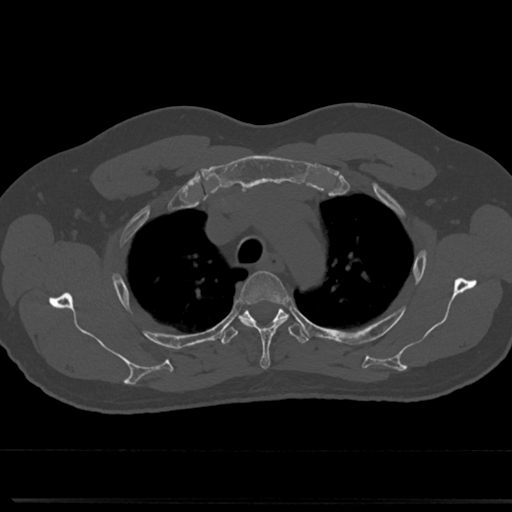
CT including the spine, one axial slice; slice 571 of 817 in the series (ordered by position); 120 kVp; bone window (W 1800 / L 400 HU); 0.5 mm slice thickness; 512 × 512 image matrix, field of view 355 × 355 mm. Patient: male, 61 years. From the clinical record (not read from this slice): primary cancer: prostate.
Structures marked on this image (semi-automatically segmented with operator editing):
- T3 vertebra: bounding box [x1, y1, x2, y2] px = [241, 270, 285, 369]
- T4 vertebra: [219, 301, 310, 345]